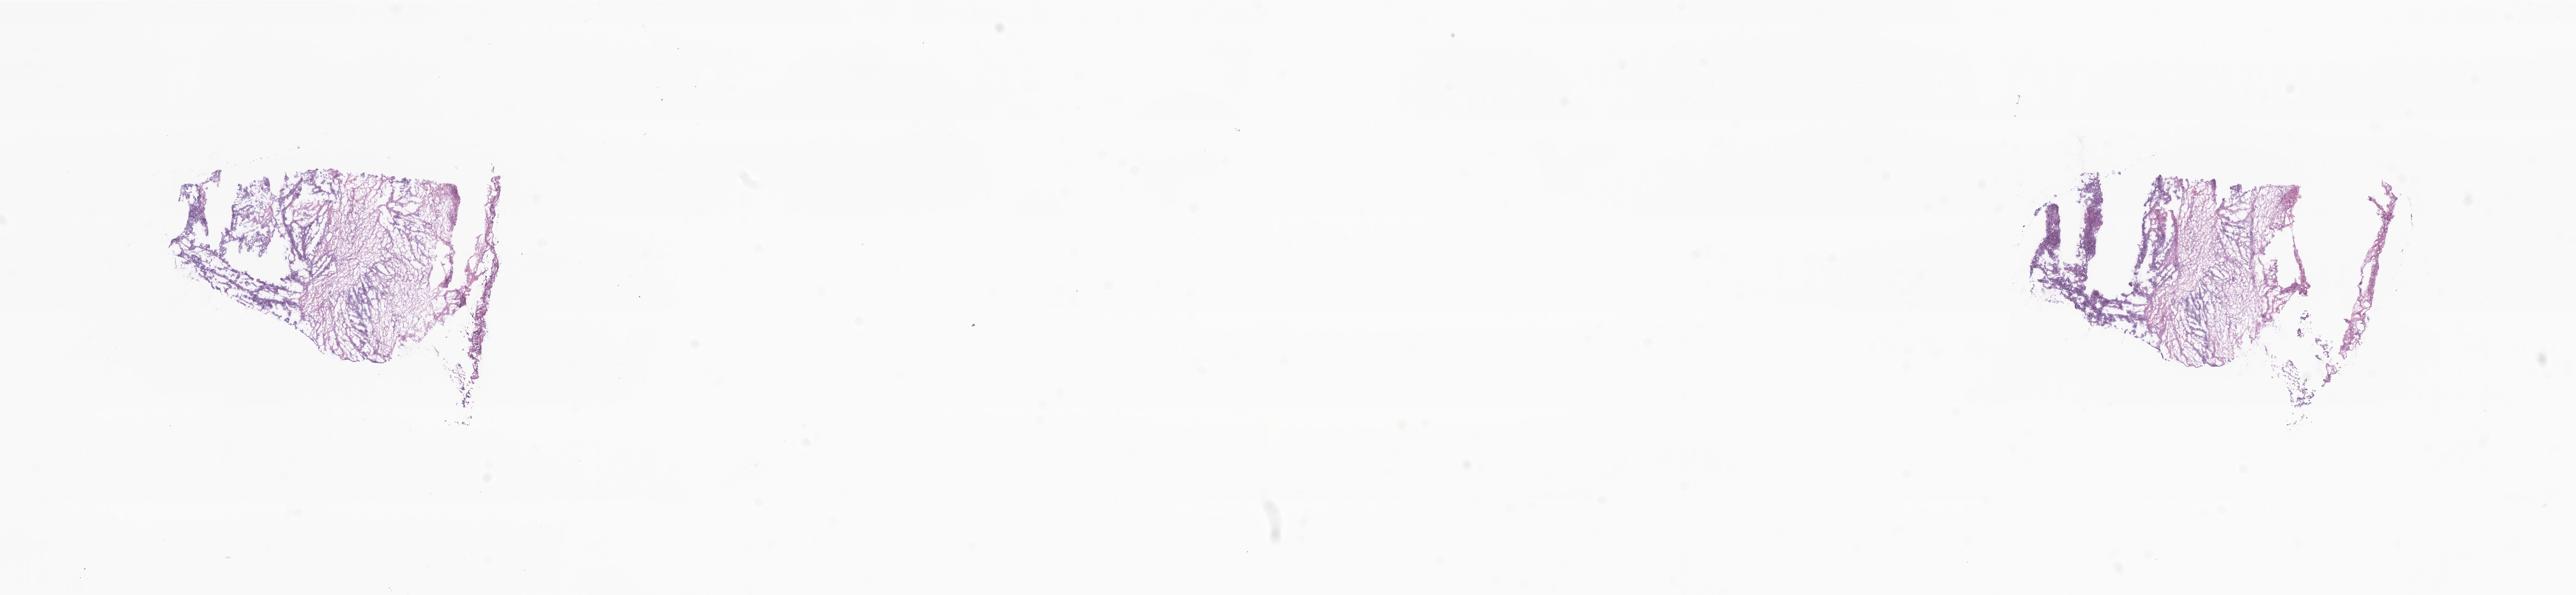
Digitized hematoxylin and eosin (H&E)-stained section — a low-resolution overview of the entire scanned area, about 28.8 x 6.7 mm, frozen section (tissue freezing medium), specimen: metastatic tumor tissue. Patient sex: female. Slide review estimates, as recorded: tumor cells 50%, tumor nuclei 48%, stromal cells 5%, necrosis 5%, normal cells 40%. Inflammatory infiltration, as recorded: lymphocyte infiltration 0%, monocyte infiltration 0%, neutrophil infiltration 0%.
Patient diagnosis (primary): Serous surface papillary carcinoma. Section: bottom of the tissue portion.